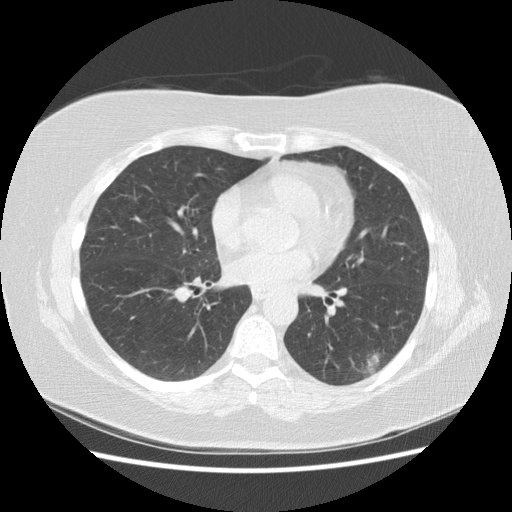
Chest CT (low-dose screening protocol), one axial image; third screening round (two years after baseline); lung window (W 1500 / L -600 HU); 120 kVp; slice 73 of 151 in the series. Female participant, aged 57 years at enrolment. Current smoker at enrolment.
• Expert reader's lesion annotation, bounding box <337,323,406,389> (left, top, right, bottom; pixels).
• Reader record for this screening exam (exam-level; its link to the box is not recorded): non-calcified nodule or mass ≥4 mm, left lower lobe, 40 × 20 mm, poorly defined margins, mixed attenuation, pre-existing on the prior screen: yes; interval growth: yes.
• Official screen result: positive, other.
• Participant outcome: lung cancer diagnosed 55 days after this screen — squamous cell carcinoma, NOS, left lower lobe, poorly differentiated (G3), stage IB (AJCC 6th edition), 40 mm at pathology.